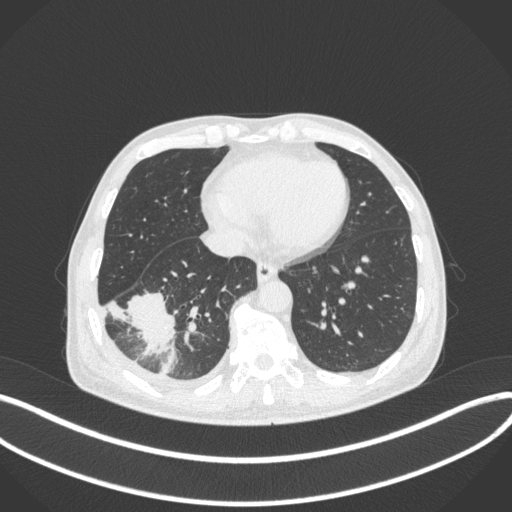
Chest CT, one axial slice; position 118 of 385 along the scan axis; reconstruction kernel B31f; 120 kVp; lung window (W 1500 / L -600 HU); 1 mm slice thickness; 512 × 512 image matrix, field of view 400 × 400 mm. Male patient, age 64 years. Case-level facts recorded for this patient, not image findings: clinical TNM (as recorded): T3 N0 M0.
Outlined on this slice (rectangle marked by the reading radiologist):
- lung tumour (recorded histology: adenocarcinoma): bounding box <120,283,184,379> (left, top, right, bottom; pixels)